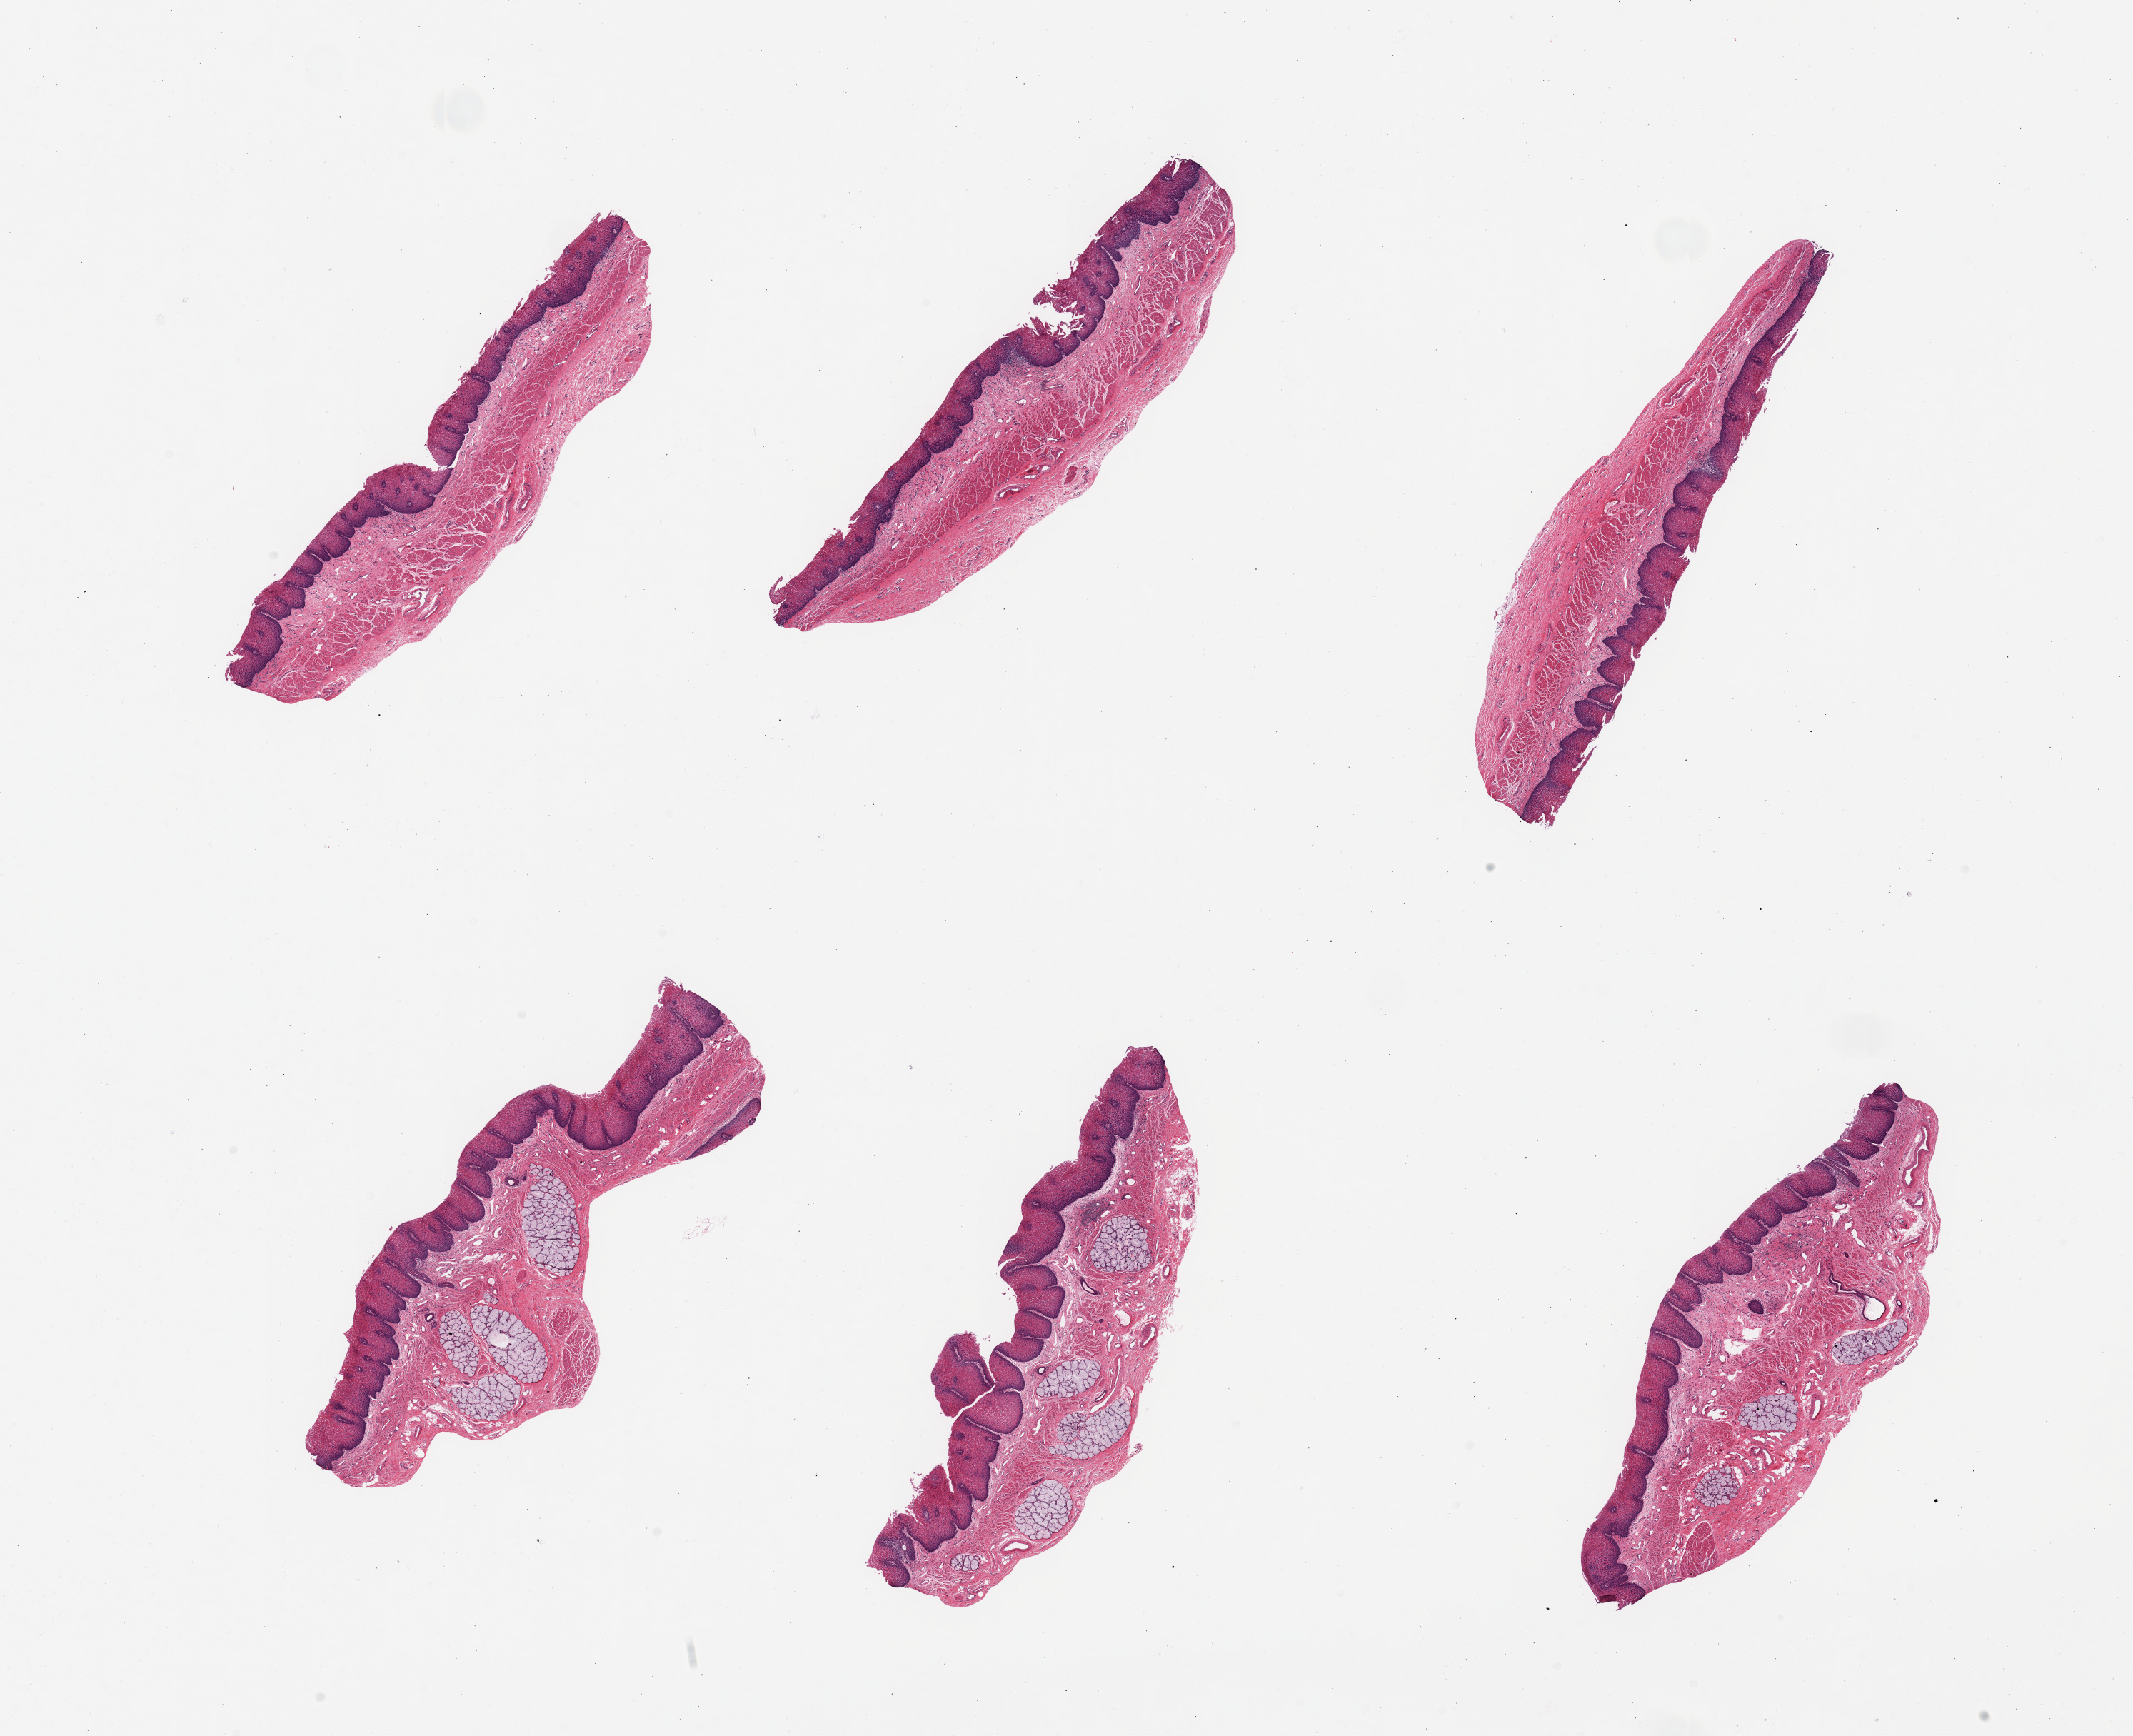
Digitized haematoxylin and eosin-stained section, brightfield, a low-resolution overview of the entire scanned area, about 23.6 x 19.2 mm; PAXgene-fixed, paraffin-embedded tissue; sampled site (target tissue): esophageal mucous membrane; tissue donor sample. Donor sex: male.
Reviewer comment on this tissue sample: 6 pieces; focal superficial desquamation of stratified squamous epithelium; ~0.4mm thick epithelium; submucosal glands.